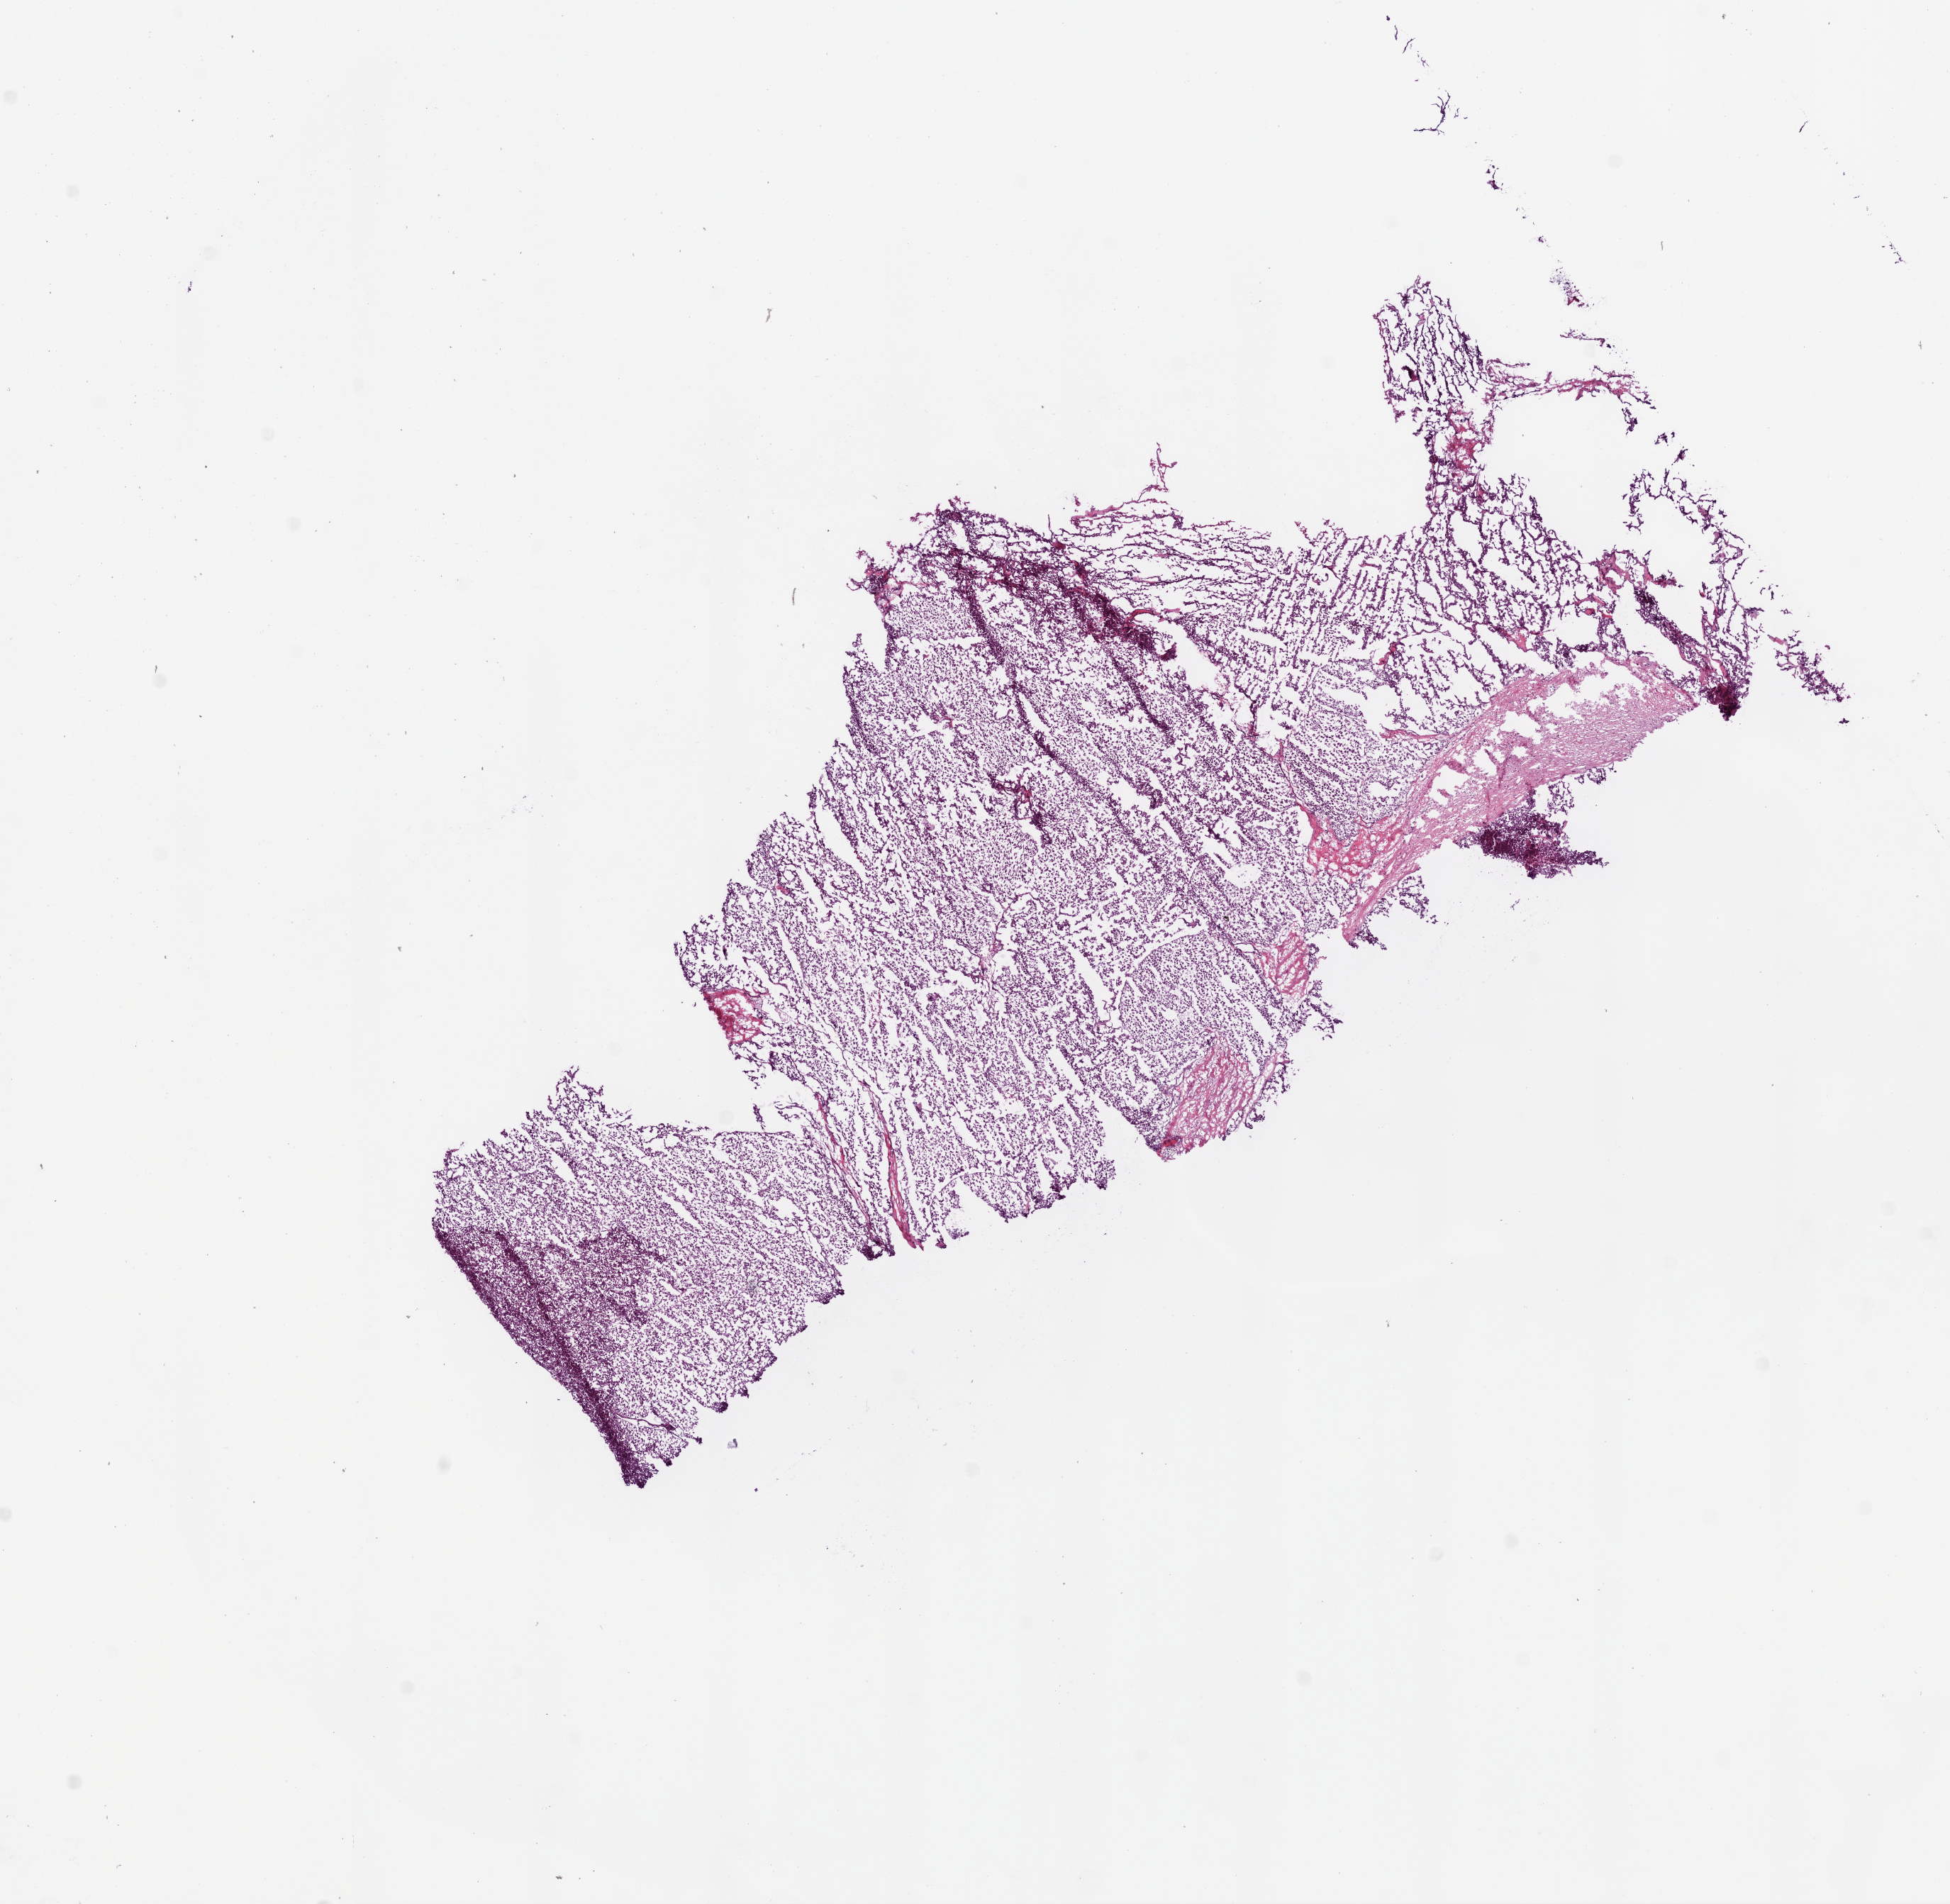
Hematoxylin and eosin (H&E) stained whole-slide image — shown as a low-resolution overview of the whole scanned area (about 11.0 x 10.8 mm). Frozen section. Kidney, primary tumour sample. Female patient; age at initial diagnosis 71 years. Histologic grade: GX (grade cannot be assessed). Composition of this section per pathologist review: tumour cells 92%, tumour nuclei 84%, normal cells 0%, stromal cells 8%, necrosis 0%.
Pathologic diagnosis: Clear cell adenocarcinoma, NOS. AJCC pathologic stage: I.